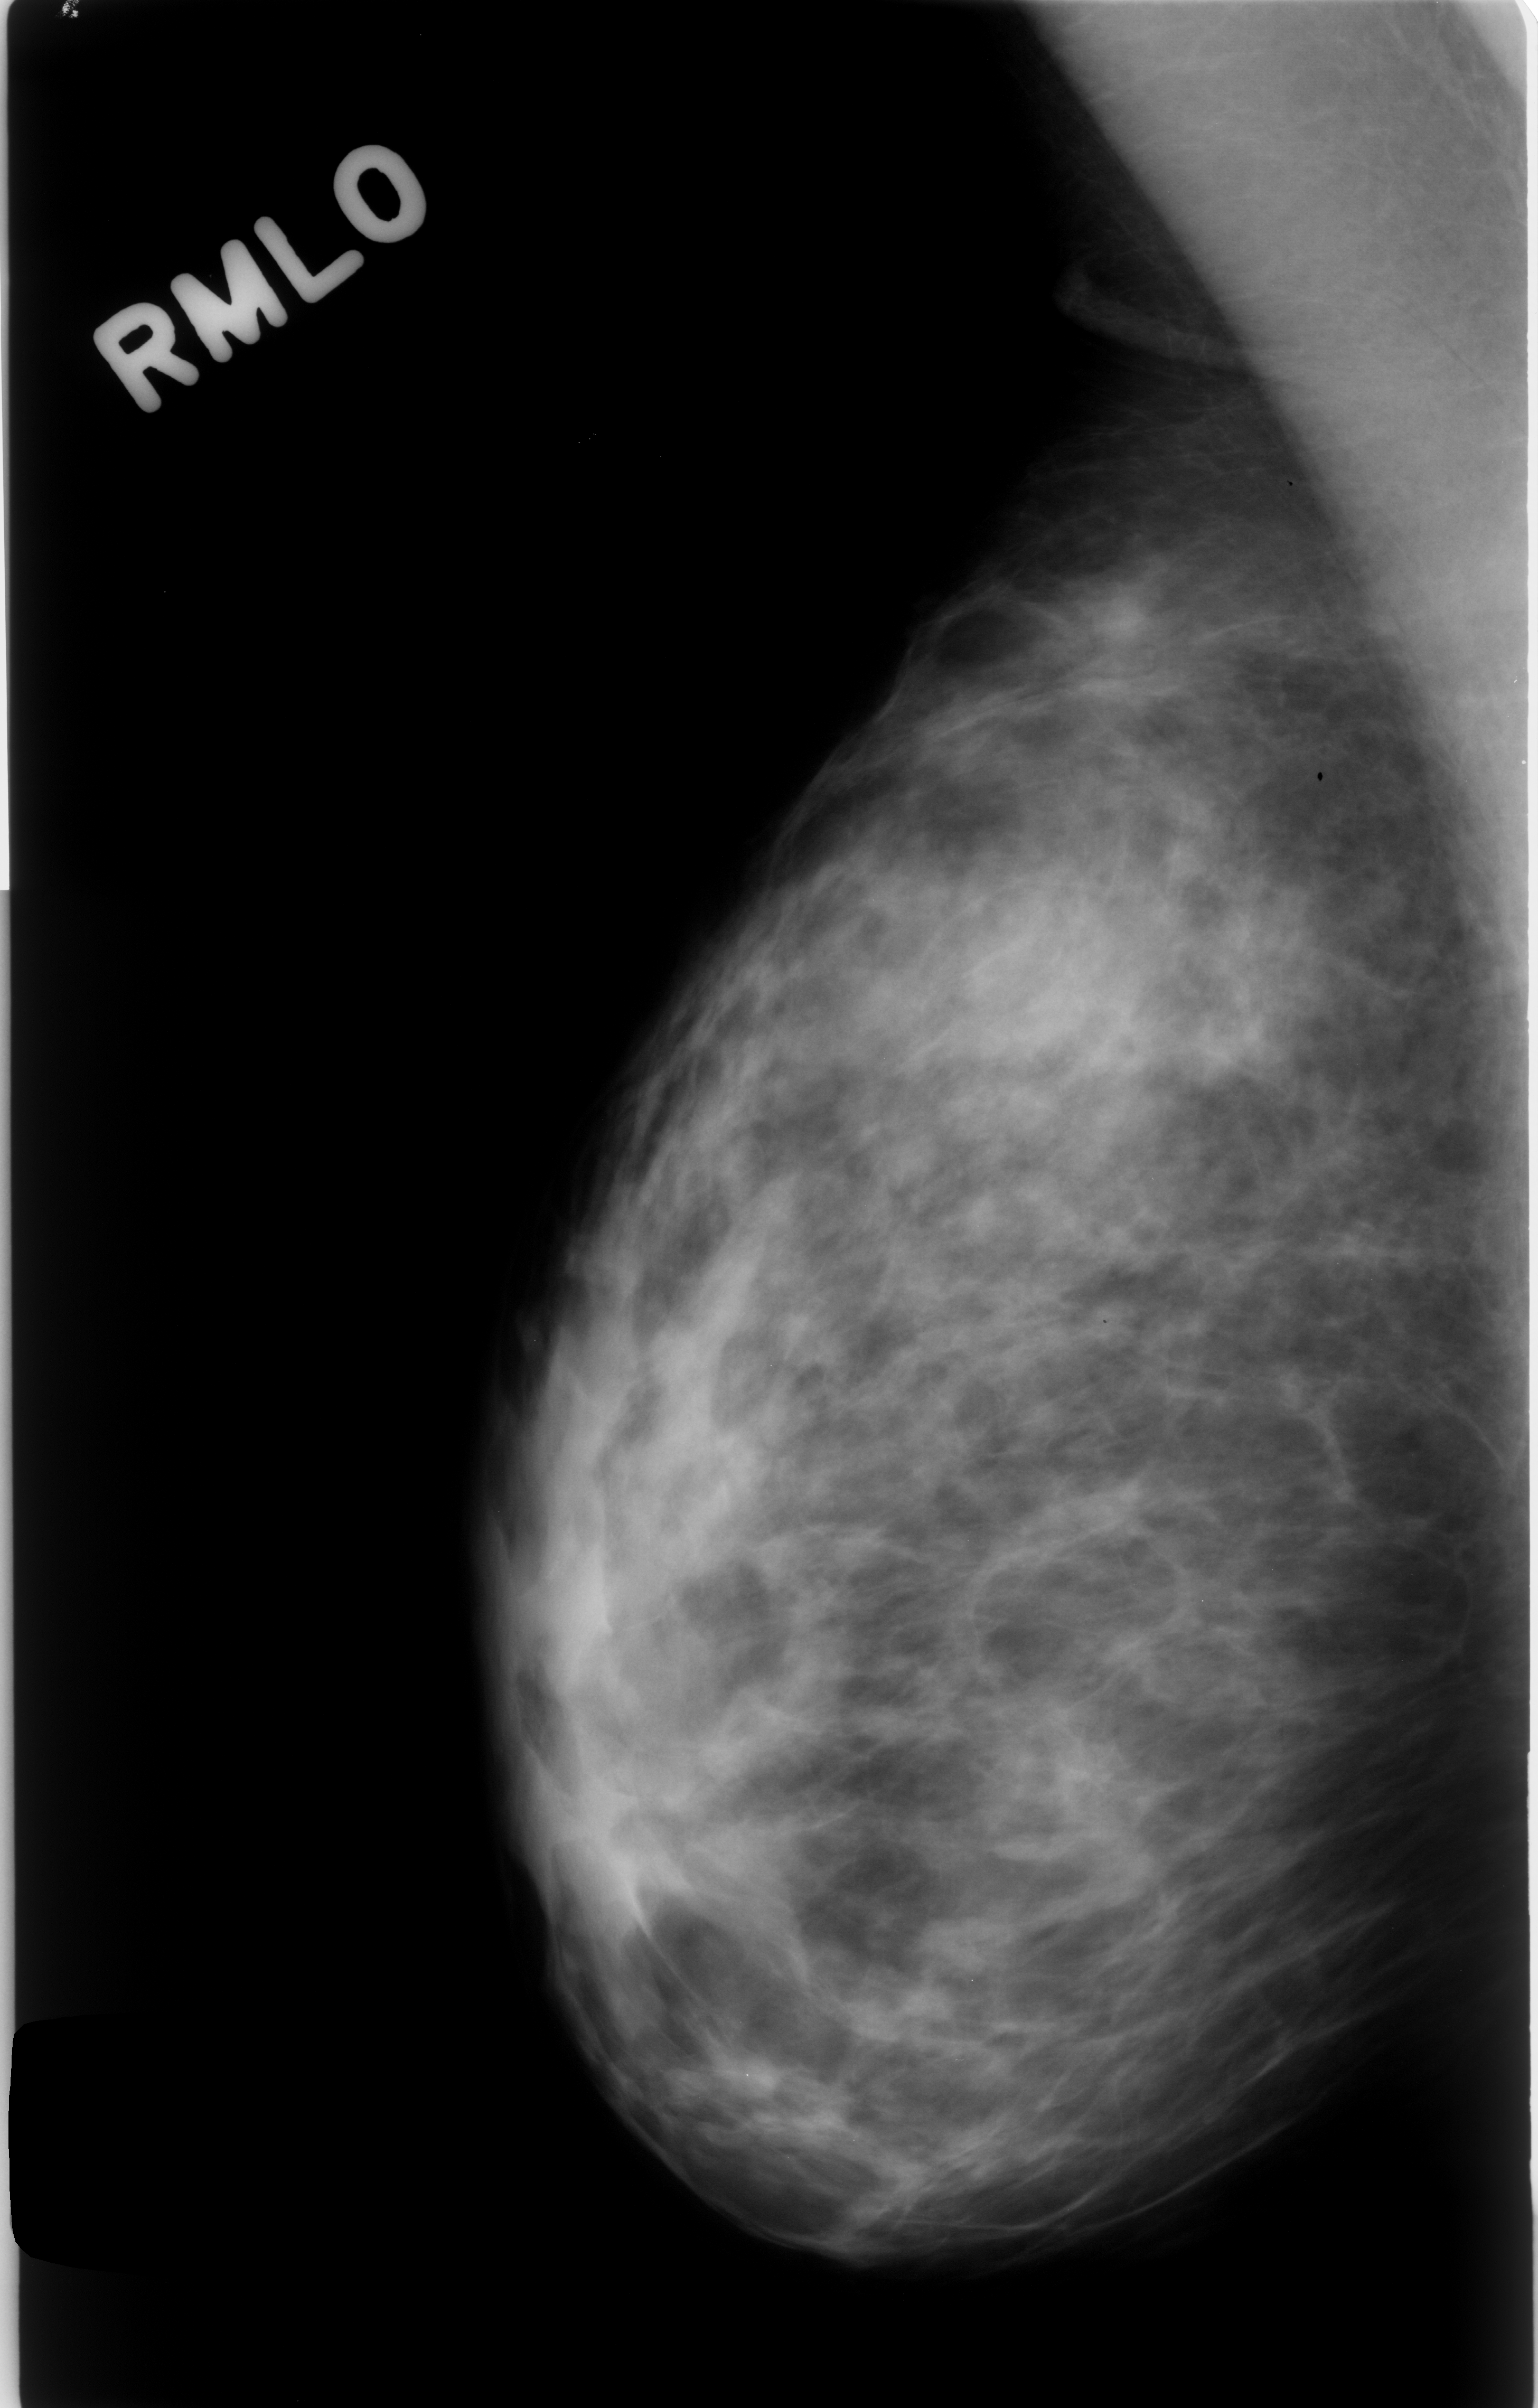
Digitized screen-film mammogram. Right breast. Mediolateral oblique (MLO) view. 1538 × 2408 image matrix.
Marked abnormalities (boxes around the expert regions of interest):
- mass, shape architectural distortion, margins spiculated; BI-RADS assessment category 4; outcome (as recorded, no biopsy): benign without callback (not worked up further): bounding box [x1, y1, x2, y2] px = [1016, 555, 1233, 760]